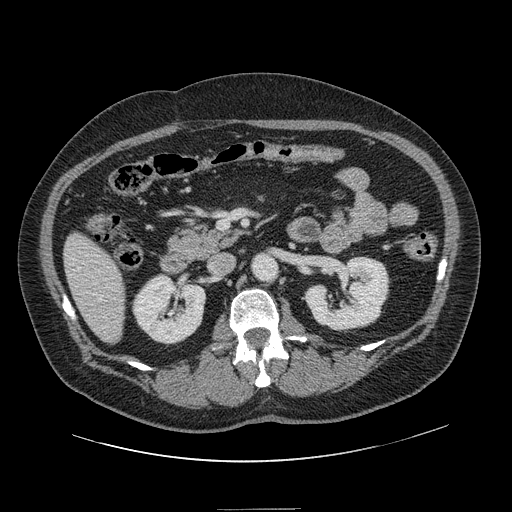
Contrast-enhanced abdominal CT, one axial slice. Position 51 of 154 along the scan axis. 120 kVp. Intravenous contrast given. Soft-tissue window (W 400 / L 40 HU). 2.5 mm slice thickness. 512 × 512 image matrix, field of view 451 × 451 mm. Male patient, age 61 years. Case-level facts recorded for this patient, not image findings: diagnosis: colorectal cancer liver metastases, imaged before liver resection; multiple liver metastases: yes; largest metastasis: 2.6 cm; disease in both lobes: yes.
Outlined on this slice (manually delineated by an expert):
- hepatic veins: bounding box [x1, y1, x2, y2] px = [77, 267, 102, 301]
- liver: [65, 234, 124, 343]
- planned liver remnant (the part of the liver to remain after resection): [65, 234, 124, 343]